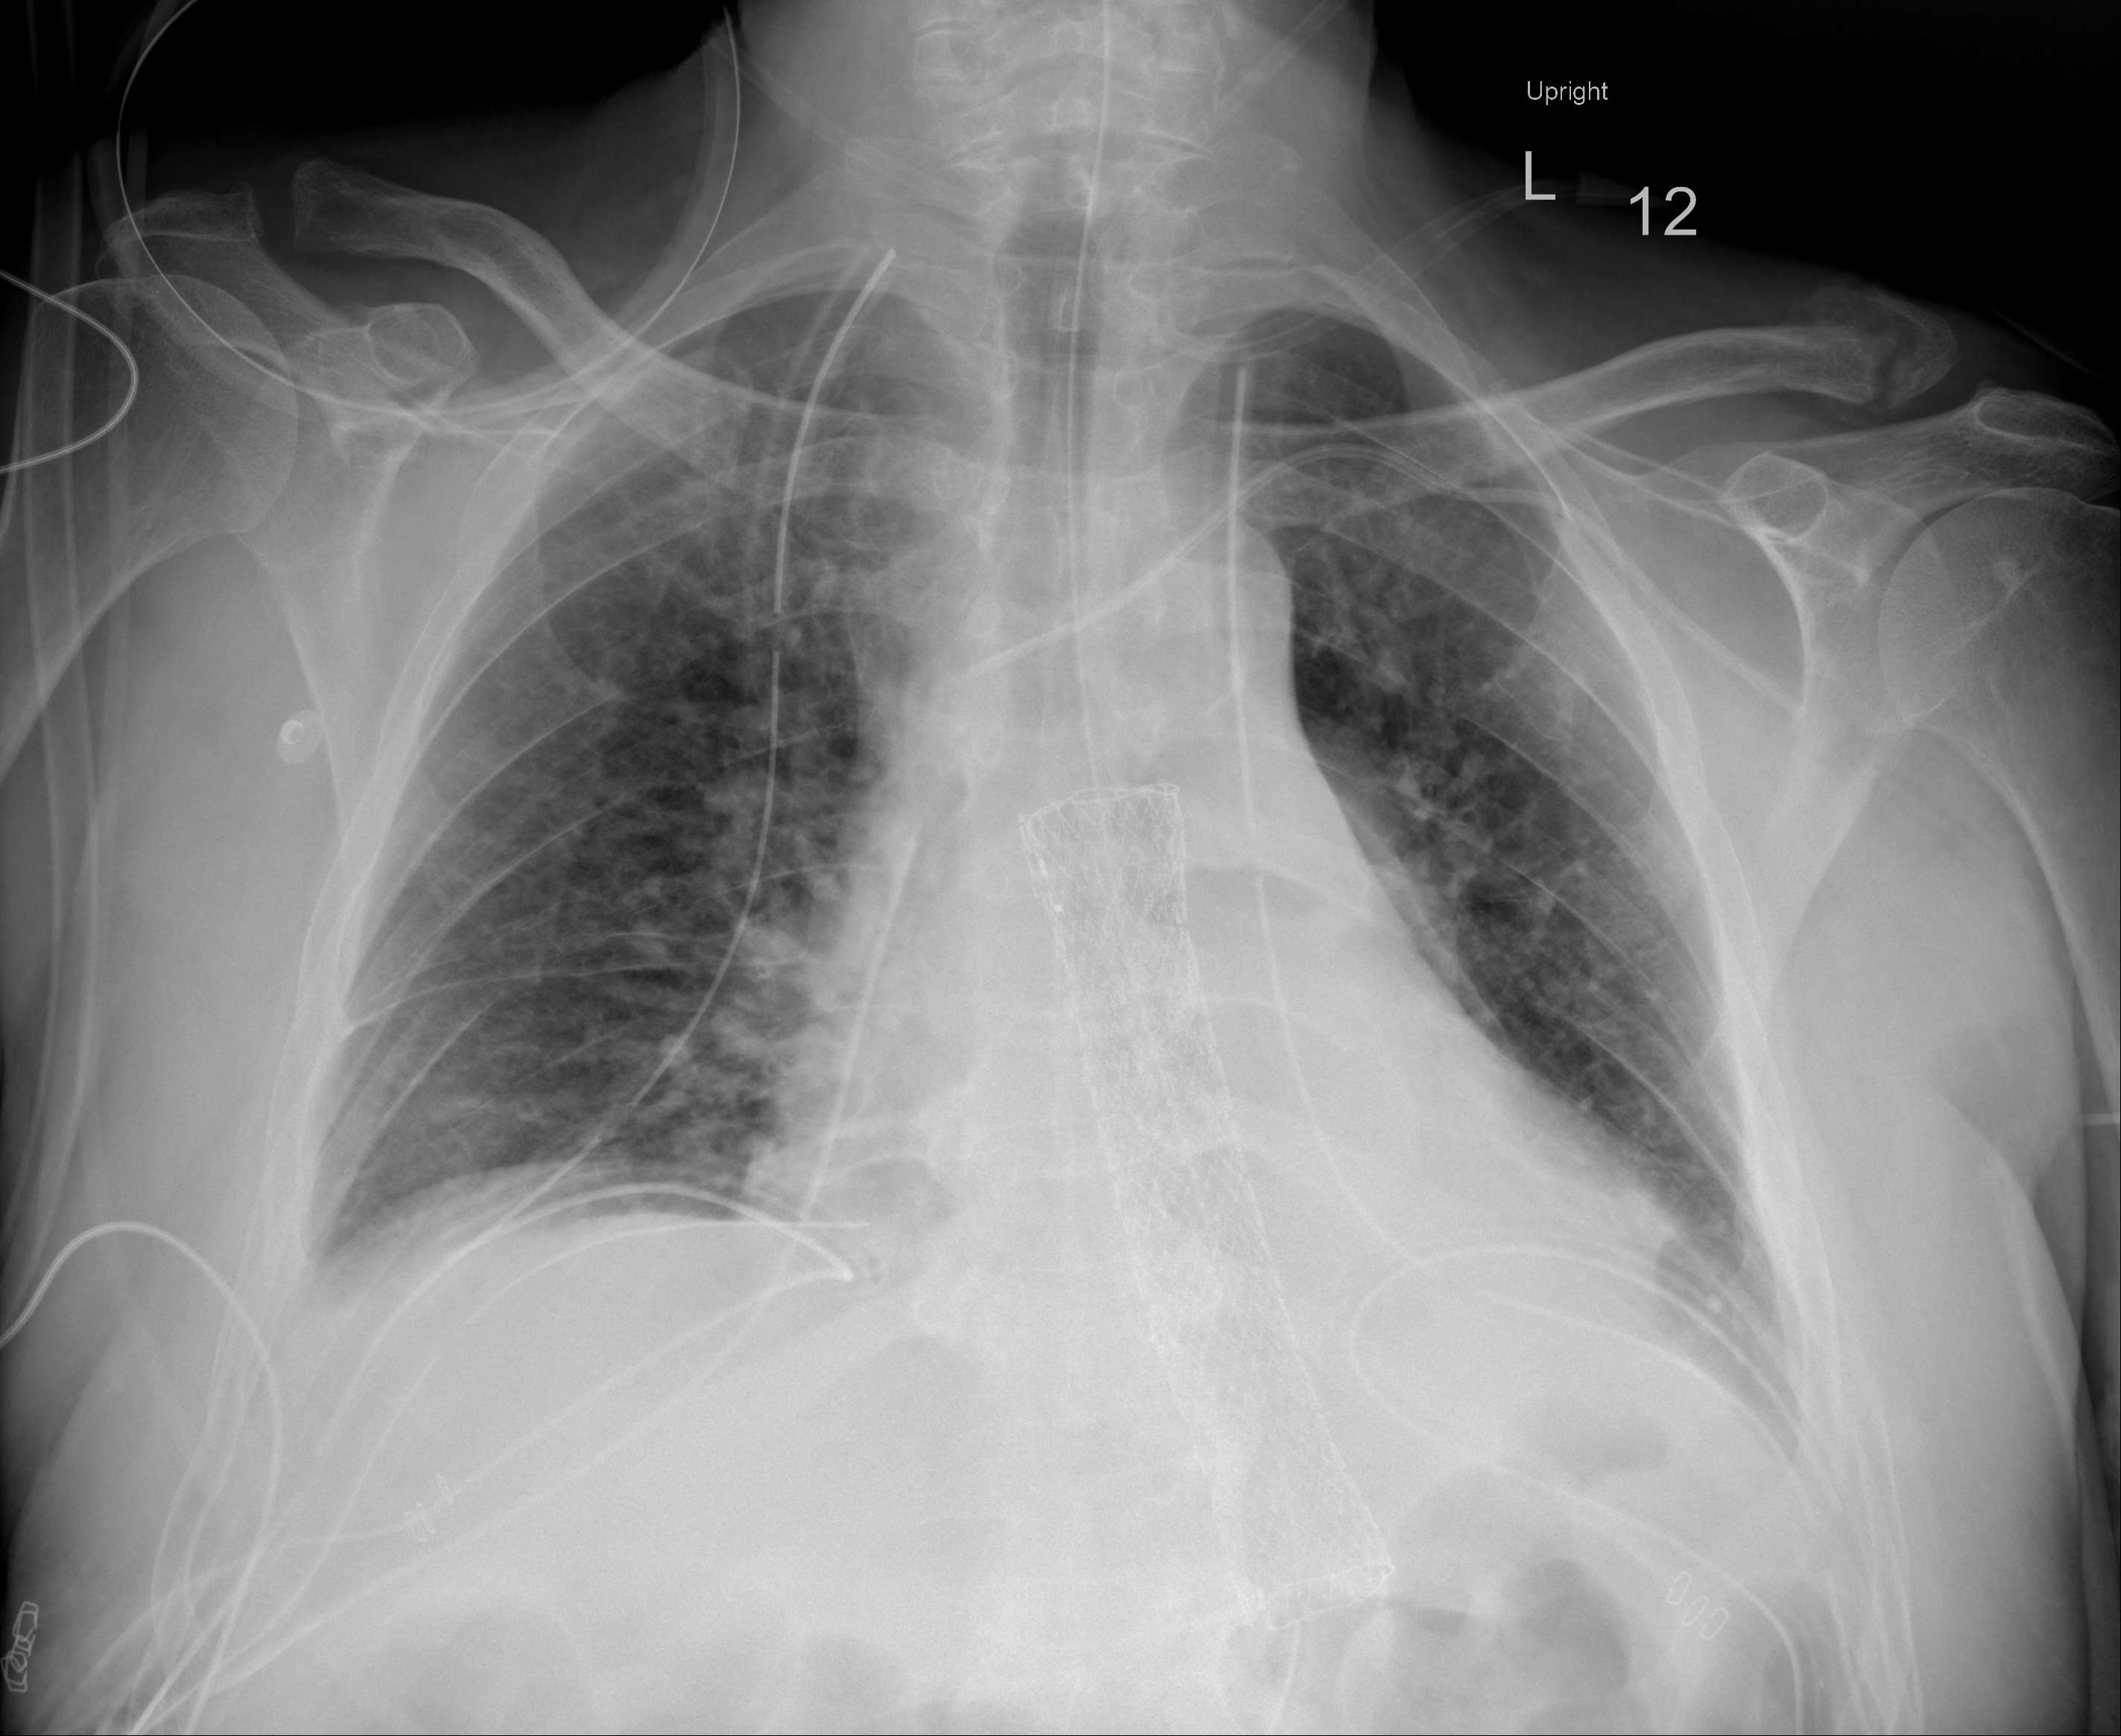
Chest X-ray (portable), AP projection. Male patient, age 64 years; imaged 2 days after the COVID-19 diagnosis.
Radiologist's key findings for this exam: Evidence of bibasilar atelectasis . There is also blunting of the CP angles indicative of small effusions.